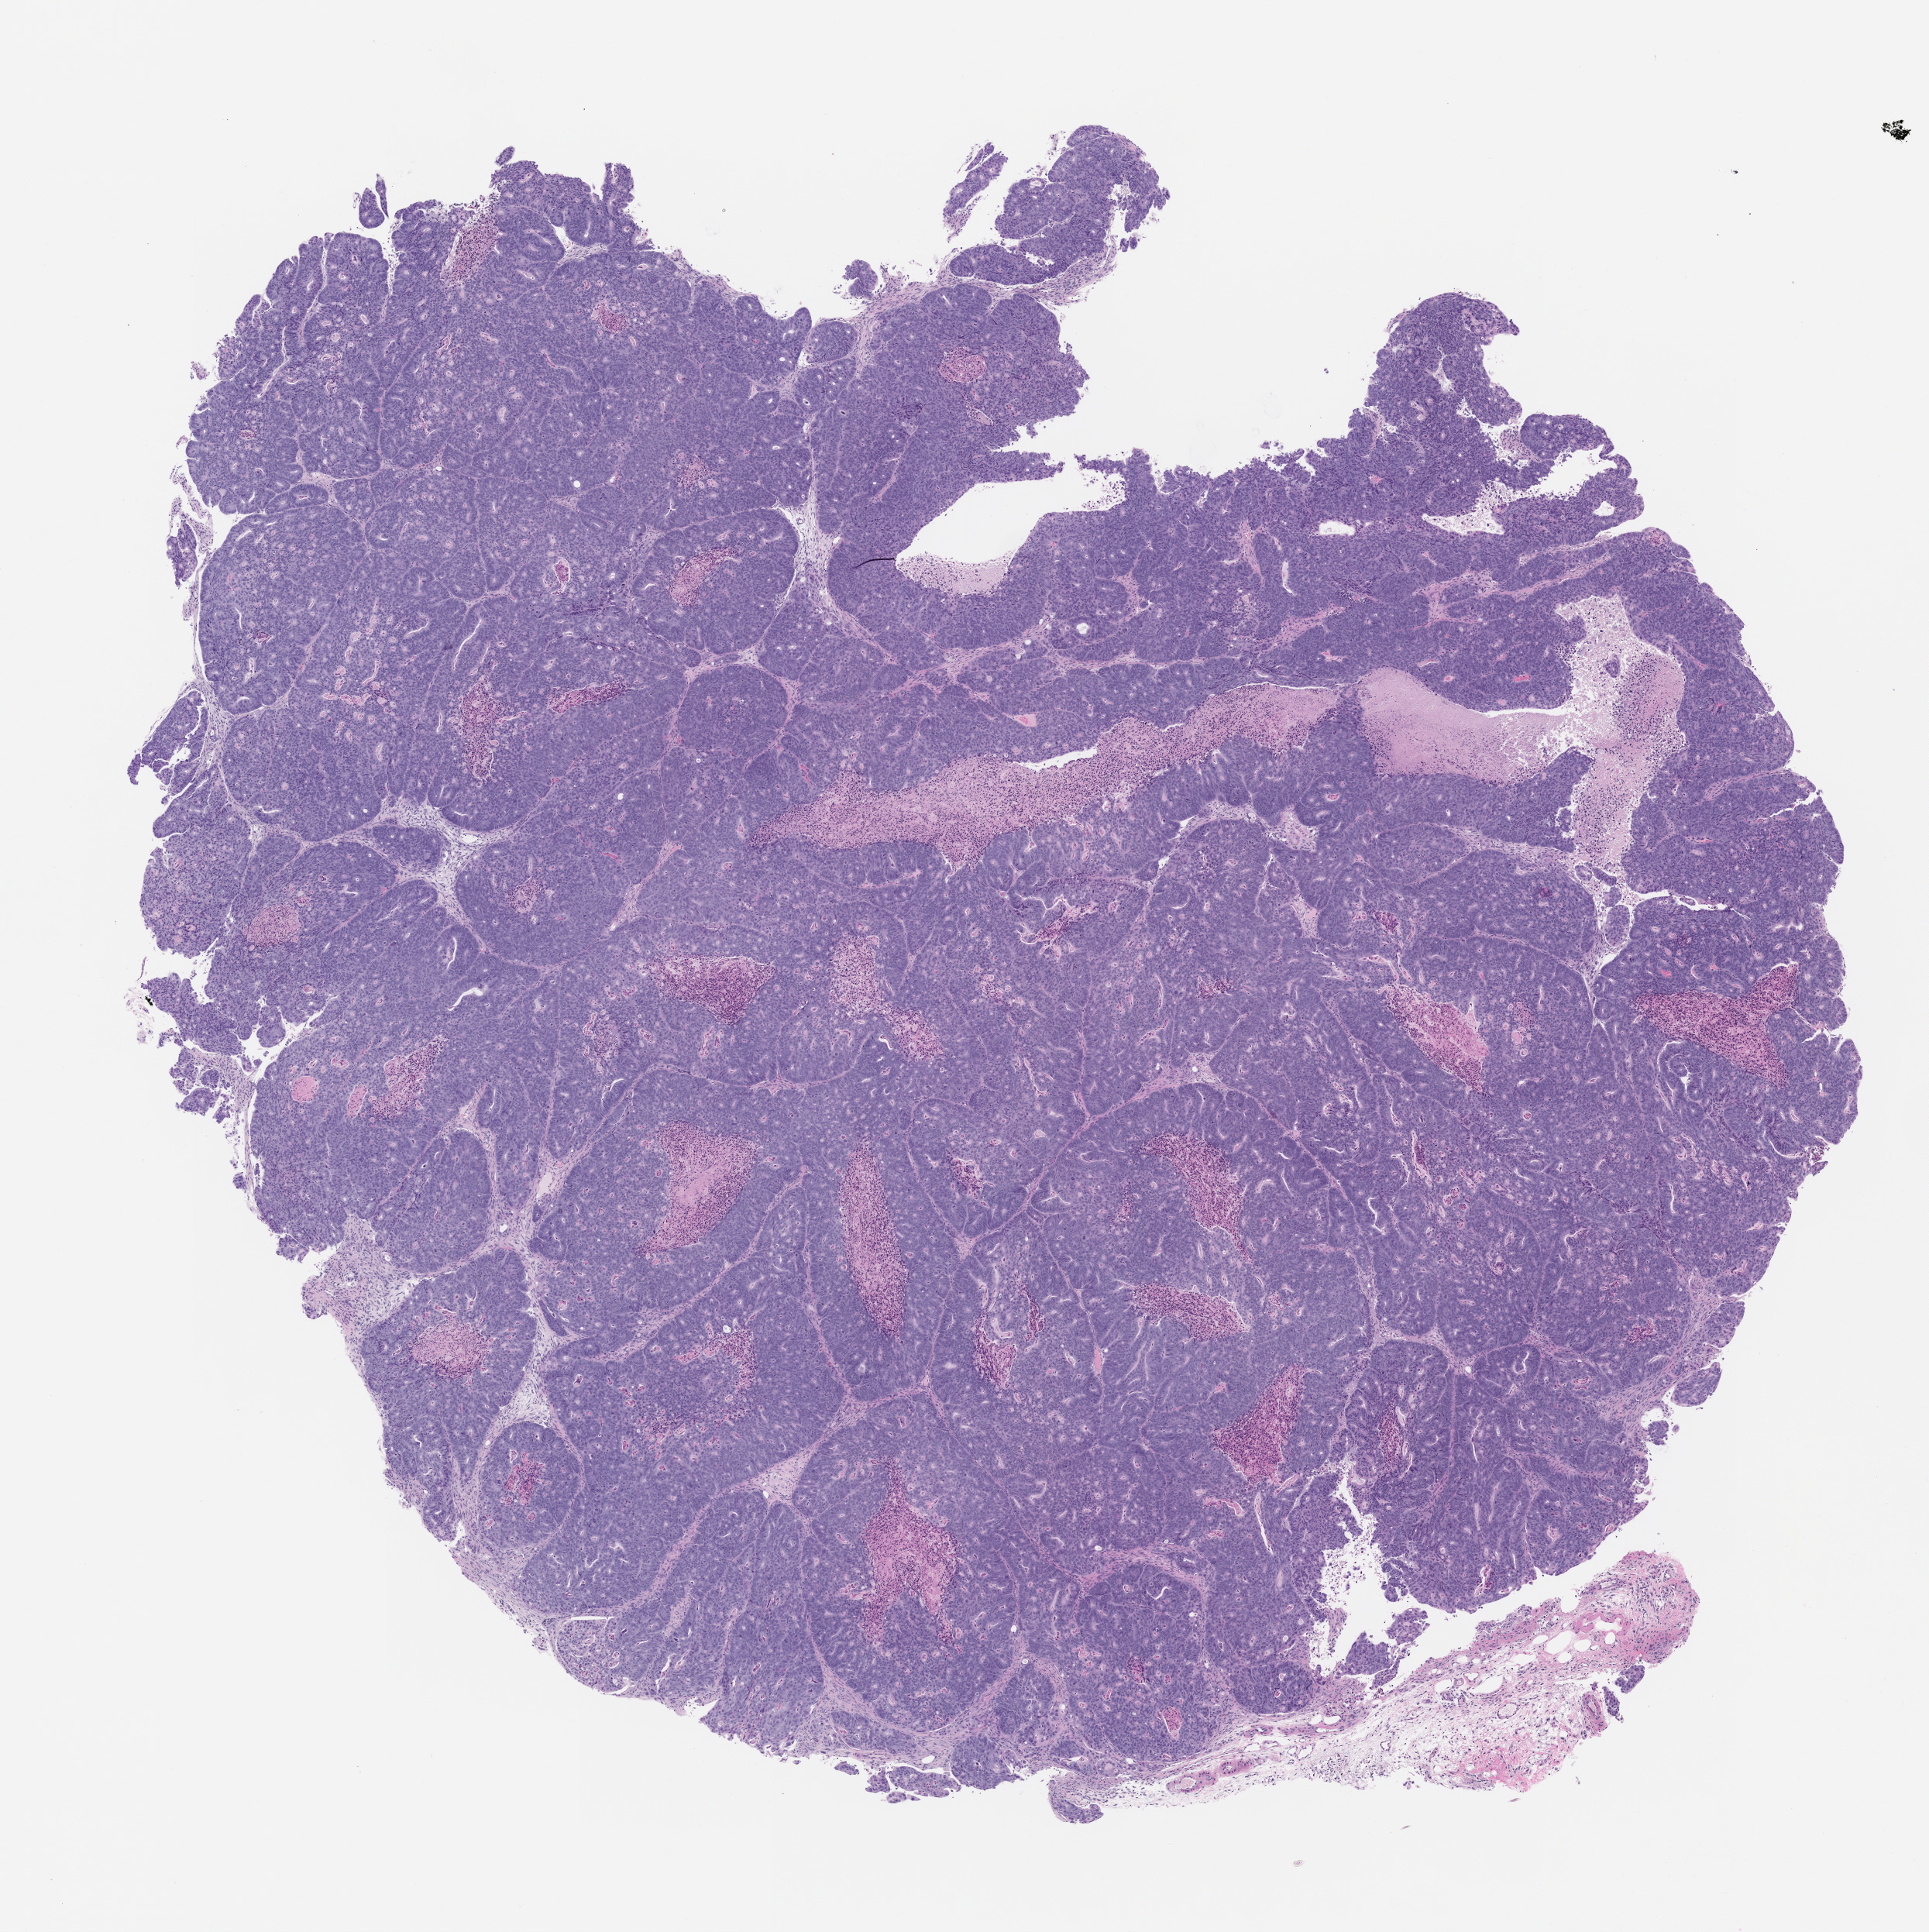
Whole-slide image, hematoxylin and eosin (H&E): patient-derived xenograft (human tumor grown in a mouse), passage 2, whole scanned area (about 10.0 x 10.0 mm) shown as a low-resolution overview, formalin-fixed, paraffin-embedded (FFPE) tissue, tumor site category: colon.
Originating patient diagnosis: Colon Adenocarcinoma.